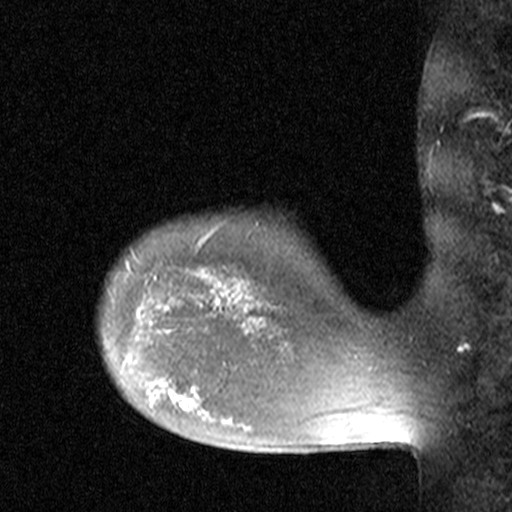
Breast MRI (dynamic contrast-enhanced), one sagittal slice; slice 36 of 44 in the series (ordered by position); dynamic contrast-enhanced study with each time point stored as its own series, time point 2 of 3 at this slice position (early post-contrast, ordered by acquisition time); 1.5 T; TE 4.5 ms, TR 11 ms; 512 × 512 image matrix, field of view 200 × 200 mm. Female patient, age 38 years. From the clinical record (not read from this slice): setting: breast cancer imaged before/during neoadjuvant chemotherapy; receptor status: HR-positive, HER2-negative.
Structures marked on this image (semi-automatically segmented with operator editing):
- analysis volume of interest (the breast-tissue region the enhancement analysis was run in; not a lesion): bounding box <176,272,251,349> (left, top, right, bottom; pixels)
- tumour enhancement mask (voxels above the 90 % enhancement threshold inside the analysis volume of interest): <213,283,251,331>